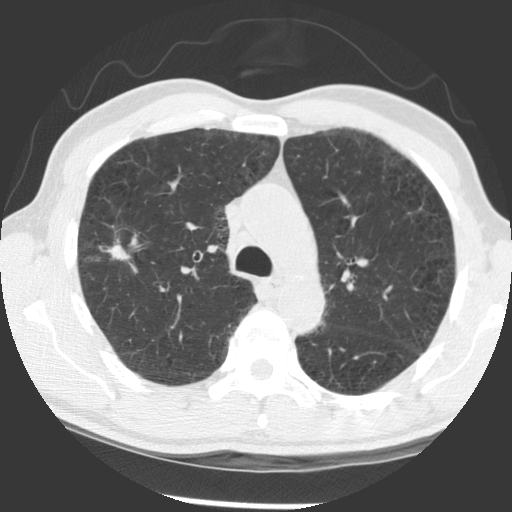
Low-dose screening chest CT, axial slice; first (baseline) screen; lung window (W 1500 / L -600 HU); slice 97 of 140 in the series; 512 × 512 image matrix. Male participant, aged 56 years at enrolment.
- Expert-annotated lung lesion, bounding box [x1, y1, x2, y2] px = [68, 227, 136, 282].
- The exam's reader record, not a measurement of the box and not confirmed to be the same lesion: non-calcified nodule or mass ≥4 mm, right upper lobe, 12 × 7 mm, spiculated (stellate) margins, soft tissue attenuation.
- Lung cancer was diagnosed 676 days after this screen: squamous cell carcinoma, NOS, right upper lobe, right middle lobe, moderately differentiated (G2), stage IB (AJCC 6th edition), 70 mm at pathology.